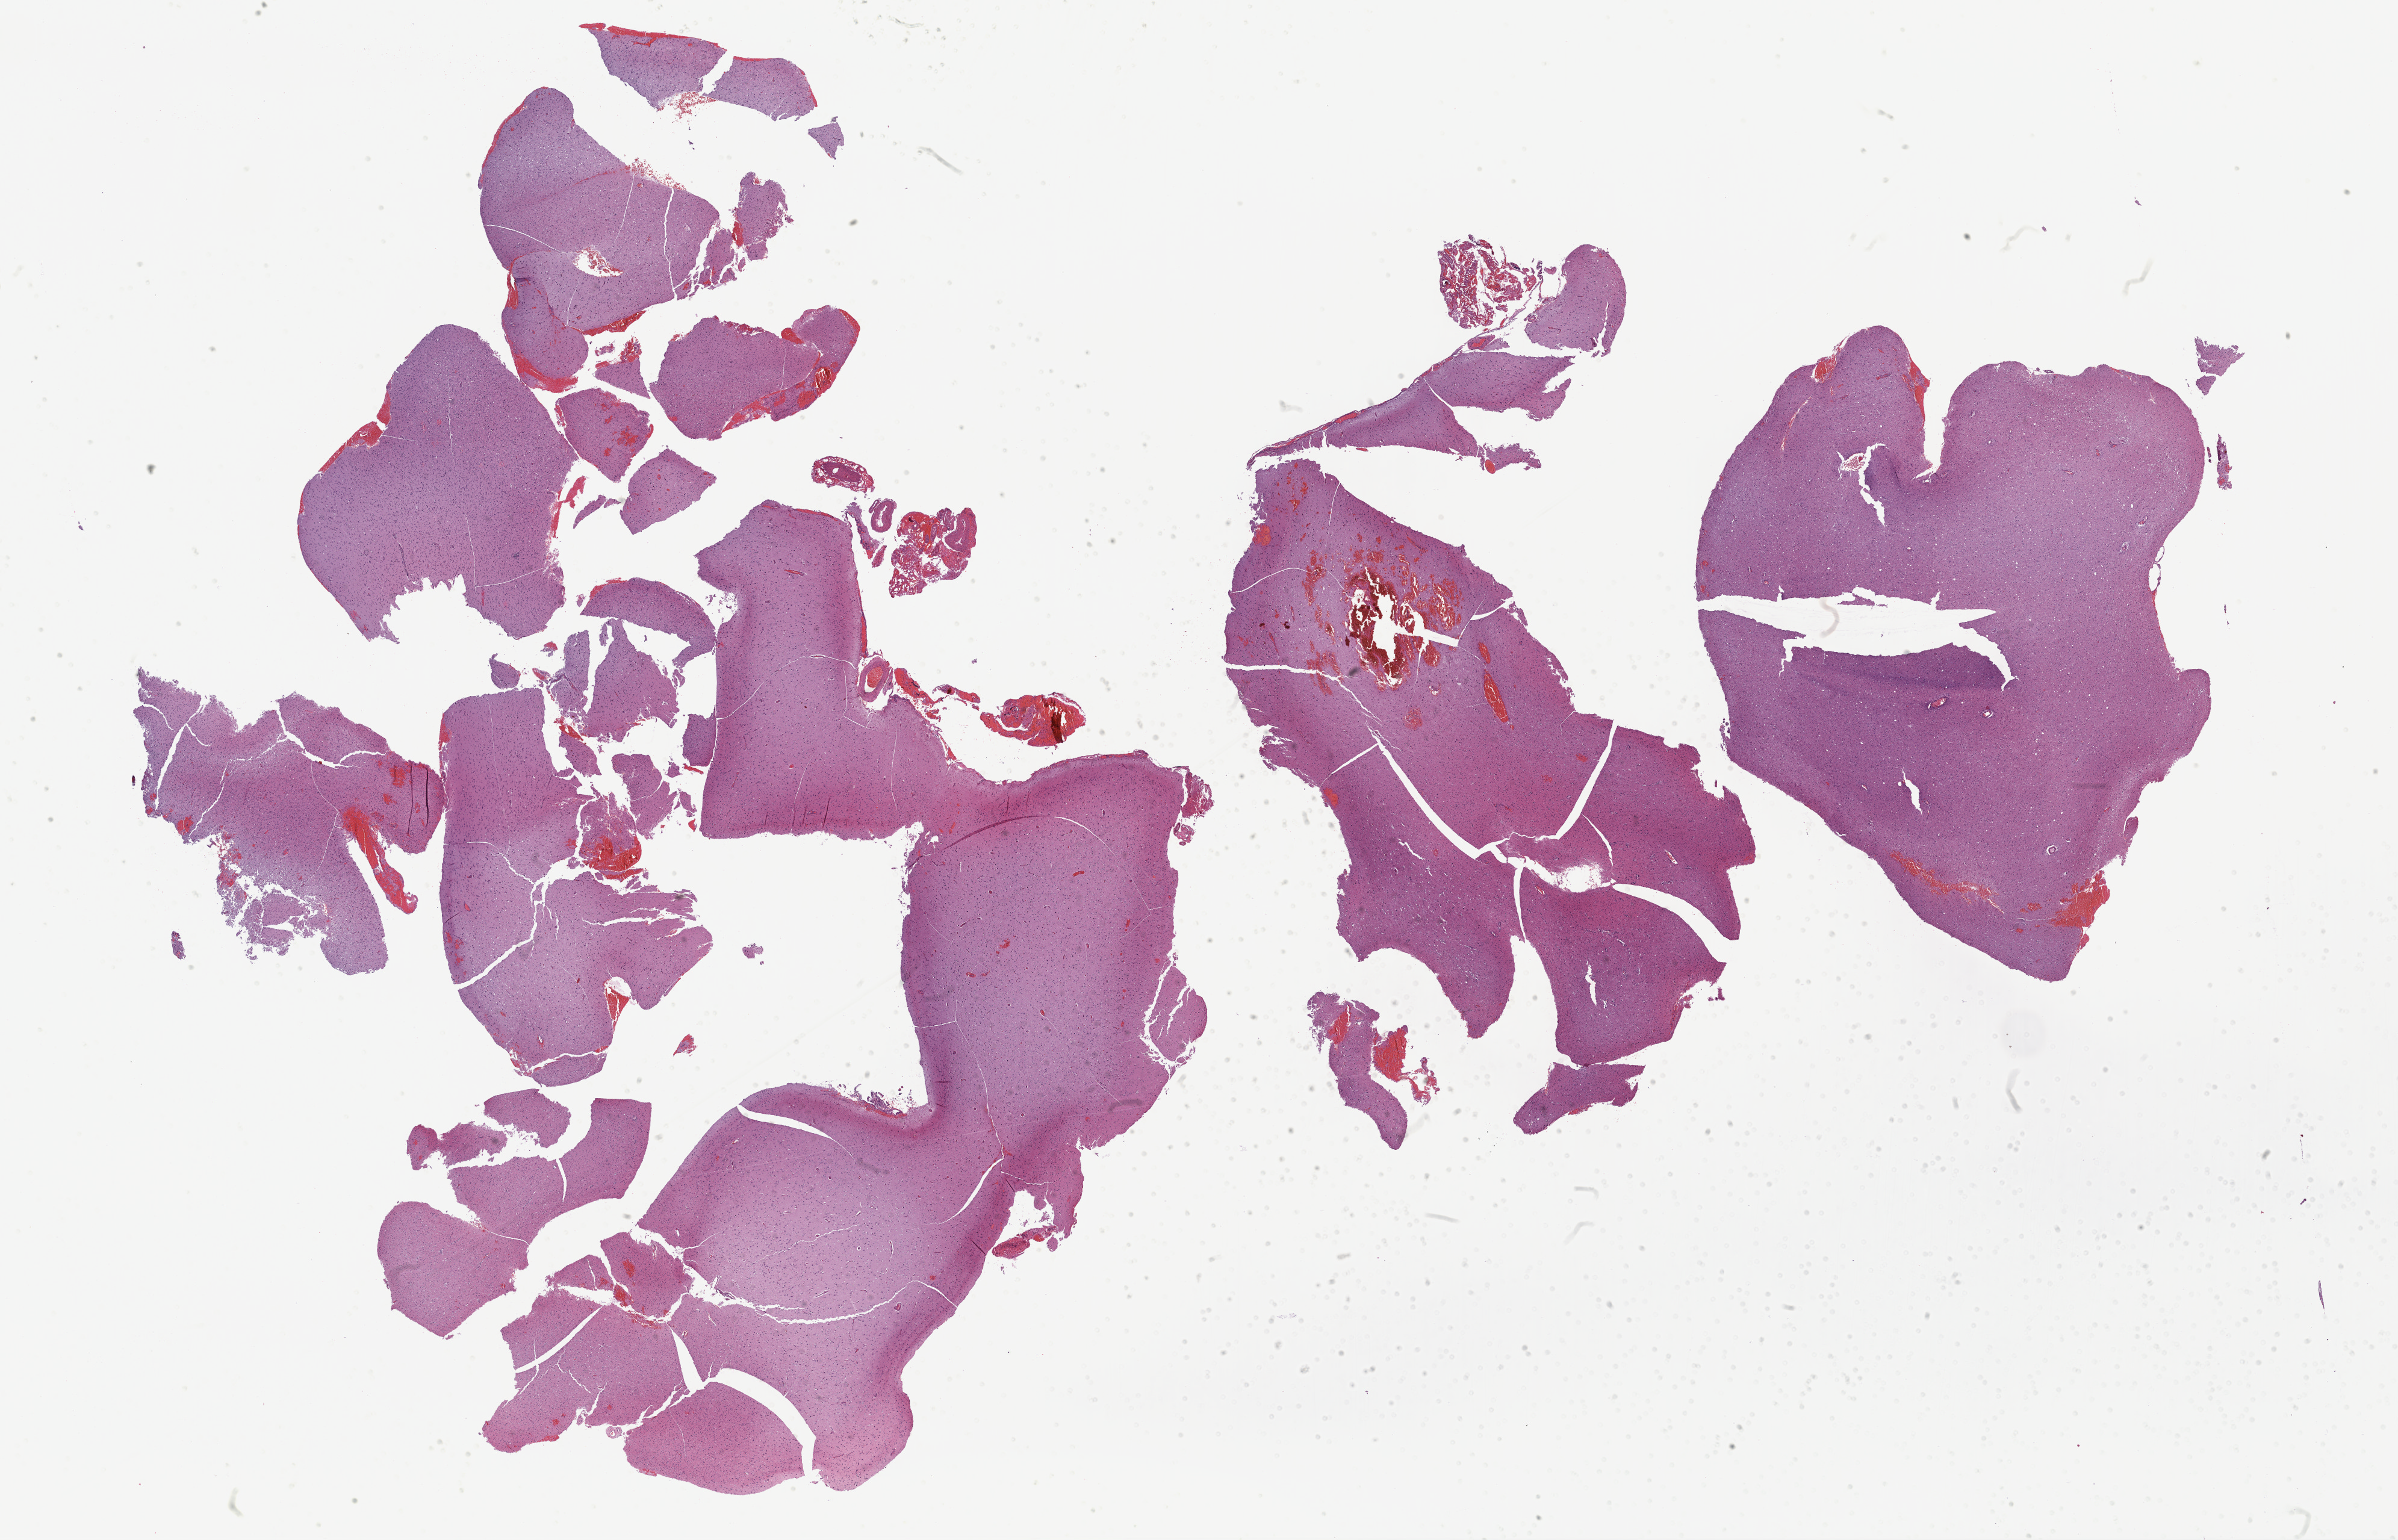
Whole-slide histology image, Hematoxylin and eosin (H&E) stained — whole scanned area (about 32.2 x 20.7 mm, slide scanned at 40x) shown as a low-resolution overview. FFPE section. Primary tumour sample from the brain. Patient: male, age at initial diagnosis 58 years.
Pathologic diagnosis: Astrocytoma, anaplastic (cerebrum).